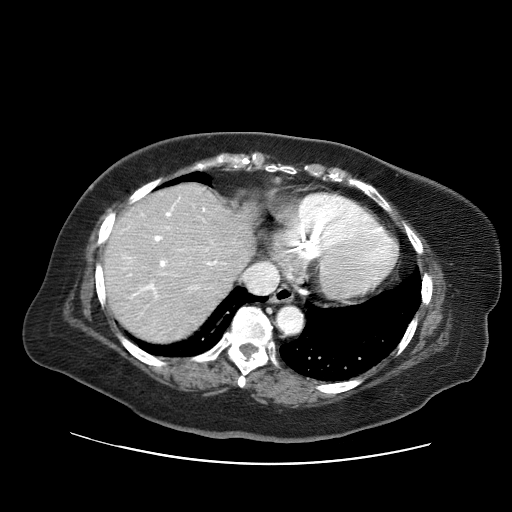
Contrast-enhanced abdominal CT (liver protocol), one axial slice. Position 54 of 71 along the scan axis. Reconstruction kernel STANDARD. 120 kVp. Soft-tissue window (W 400 / L 40 HU). 2.5 mm slice thickness. 512 × 512 image matrix, field of view 400 × 400 mm. From the clinical record (not read from this slice): diagnosis: hepatocellular carcinoma (patient treated with transarterial chemoembolisation; whether this scan precedes or follows treatment is not stated here); TNM stage (as recorded): Stage-II; Child-Pugh class: A; tumour differentiation: poorly differentiated; tumour nodularity: multinodular.
Structures marked on this image (semi-automatically segmented with operator editing):
- liver parenchyma outside the tumour (the mass and vessels are separate outlines, so this box may not span the whole liver): bounding box [x1, y1, x2, y2] px = [104, 184, 256, 342]
- liver vessels: [123, 198, 224, 298]